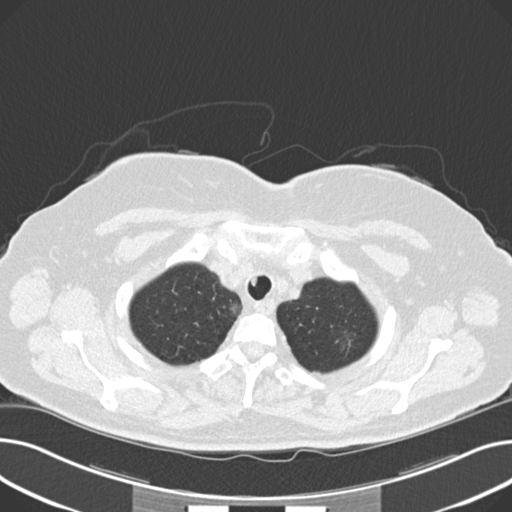
Chest CT (low-dose screening protocol), one axial image; third annual screen; lung window (W 1500 / L -600 HU); slice 32 of 203 in the series; 512 × 512 image matrix, field of view 372 × 372 mm. Female participant, aged 60 years at enrolment. Current smoker at enrolment.
Expert reader's lesion annotation, box from (x=332, y=323) to (x=377, y=363) px. The screening reader recorded 8 non-calcified nodules or masses ≥4 mm on this exam; which of them this box marks is not recorded. Official screen result: positive, other. Later outcome: lung cancer diagnosed 176 days after this screen — non-small cell carcinoma, left upper lobe, poorly differentiated (G3), stage IB (AJCC 6th edition), 7 mm at pathology.